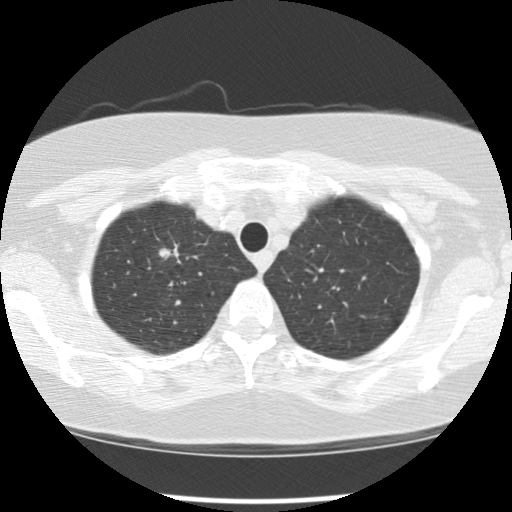
Low-dose screening chest CT, one axial slice; slice 96 of 113 in the series (ordered by position); lung window (W 1500 / L -600 HU); 2.5 mm slice thickness; 512 × 512 image matrix.
Annotated regions visible in this slice (manually delineated by an expert):
- lesion 1 (tumor, upper lobe of right lung): bounding box <159,248,174,260> (left, top, right, bottom; pixels)